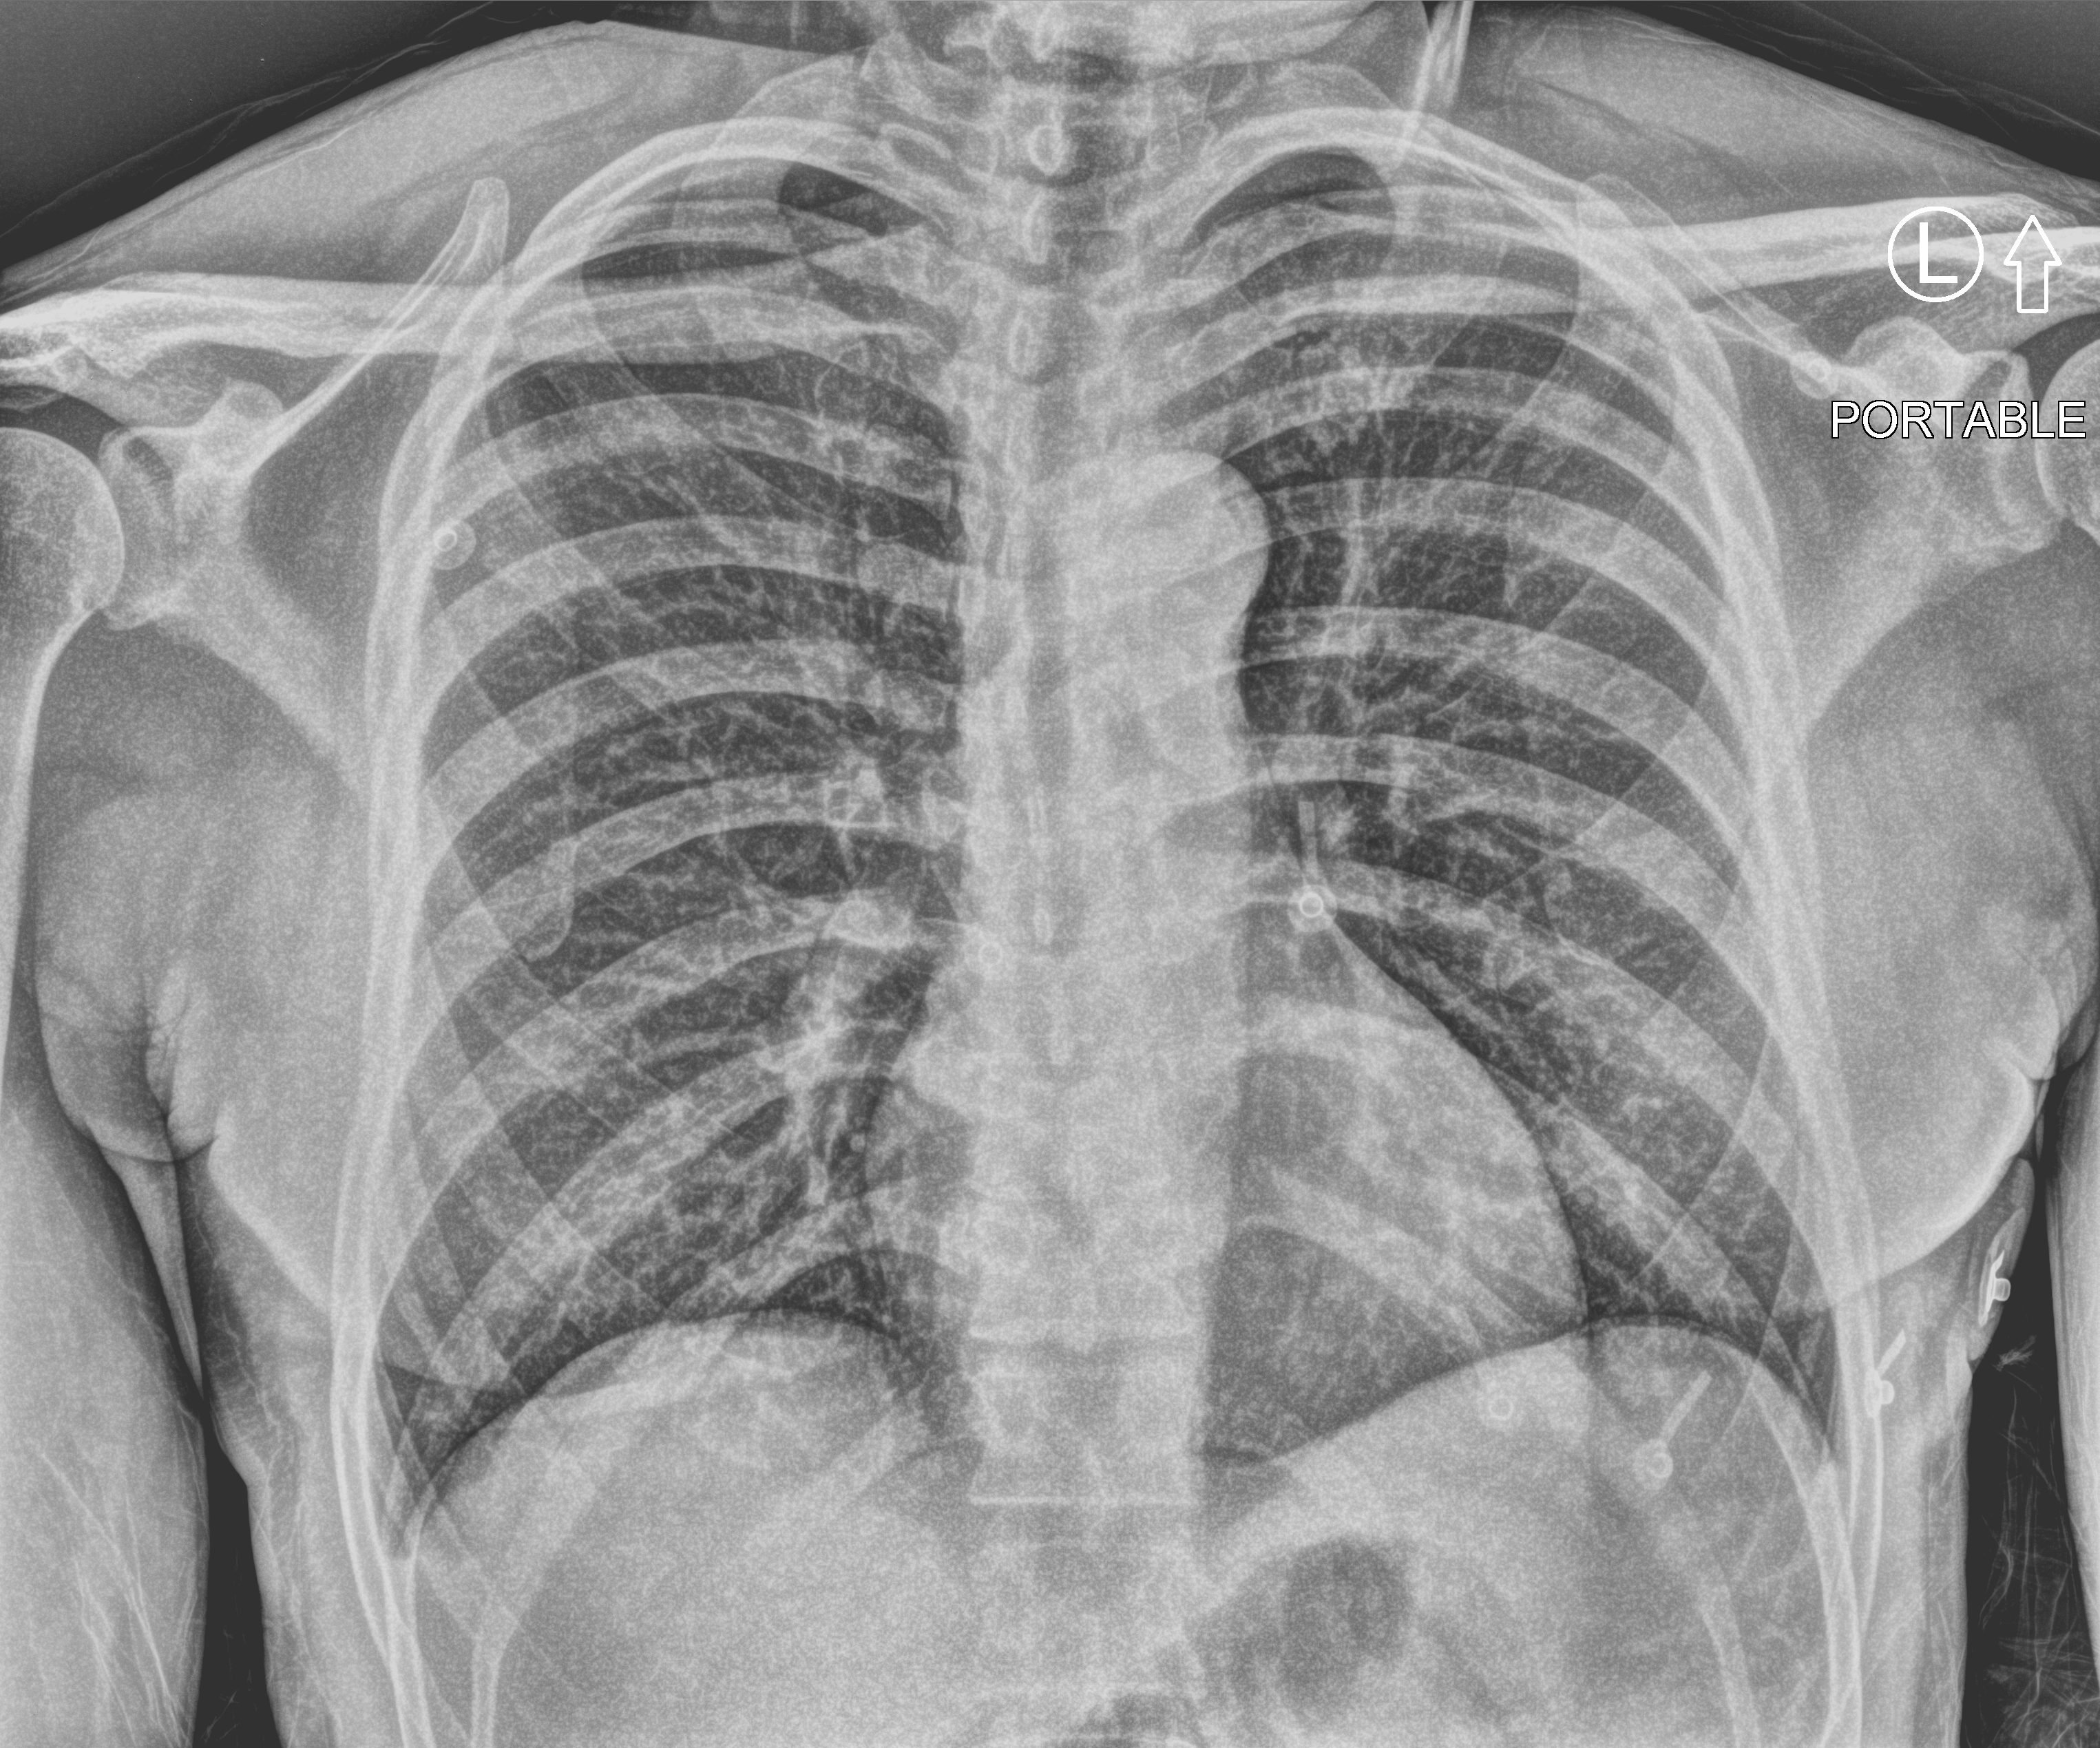
Chest X-ray (portable); anteroposterior (AP) projection. Male patient hospitalised with COVID-19, age 18–59 years.
Admission-level facts for this patient (not findings on this image; timing relative to this image not recorded): mechanically ventilated during this hospital stay: no.